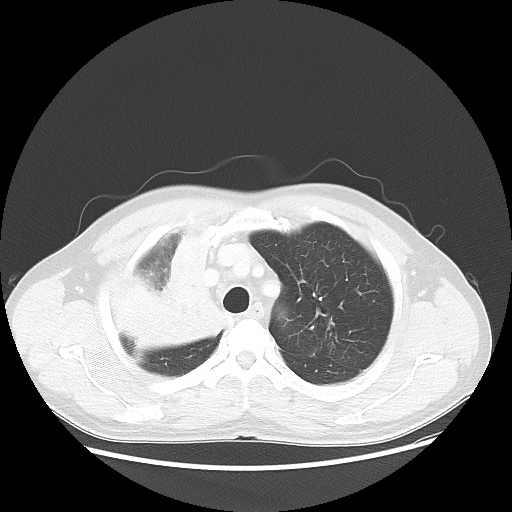
Chest CT, one axial slice; slice 43 of 56 in the series (ordered by position); 100 kVp; lung window (W 1500 / L -600 HU); 5 mm slice thickness; 512 × 512 image matrix. Male patient, age 60 years. Case-level facts recorded for this patient, not image findings: clinical TNM (as recorded): T2a N1 M0.
Annotated regions visible in this slice (bounding box drawn by a radiologist):
- lung tumour (recorded histology: squamous cell carcinoma): bounding box [x1, y1, x2, y2] px = [126, 220, 231, 363]